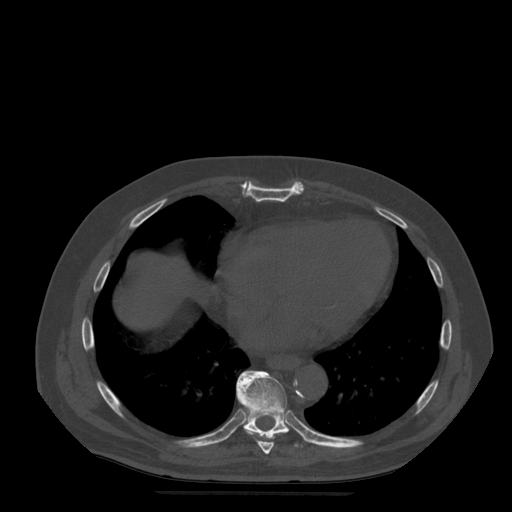
CT including the spine, one axial slice; slice 300 of 522 in the series (ordered by position); bone window (W 1800 / L 400 HU); 1.25 mm slice thickness; 512 × 512 image matrix, field of view 420 × 420 mm. Patient age 72 years. Case-level facts recorded for this patient, not image findings: primary cancer: prostate.
Structures marked on this image (semi-automatic segmentation, software-assisted and operator-edited):
- T8 vertebra: box from (x=244, y=429) to (x=285, y=455) px
- T9 vertebra: (x=236, y=371)–(x=302, y=447)